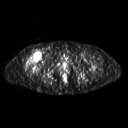
FDG PET of an extremity soft-tissue mass (from a PET/CT study), one axial slice. Position 281 of 311 along the scan axis. 128 × 128 image matrix, field of view 500 × 500 mm. Female patient, age 57 years. From the clinical record (not read from this slice): histological type: pleiomorphic undifferentiated sarcoma; grade: high; site of the primary tumour: right quadricep.
Annotated regions visible in this slice (expert contour drawn on MRI and transferred to this co-registered scan by the dataset authors):
- tumour plus oedema (research contour): bounding box [x1, y1, x2, y2] px = [25, 50, 42, 69]
- tumour (research contour): [28, 50, 42, 63]